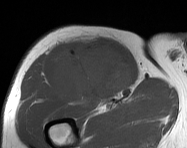
MRI of an extremity soft-tissue mass, one axial slice; position 100 of 114 along the scan axis; MR volume resampled by the dataset authors to the PET/CT grid (not the native acquisition matrix); 3.27 mm slice thickness; 187 × 148 image matrix, field of view 183 × 145 mm. Male patient. Case-level facts recorded for this patient, not image findings: histological type: pleiomorphic leiomyosarcoma; grade: intermediate; site of the primary tumour: right thigh.
Structures marked on this image (expert contour drawn on MRI and transferred to this co-registered scan by the dataset authors):
- gross tumour volume including surrounding oedema: box from (x=54, y=38) to (x=133, y=105) px
- gross tumour volume (mass): (x=54, y=38)–(x=133, y=105)